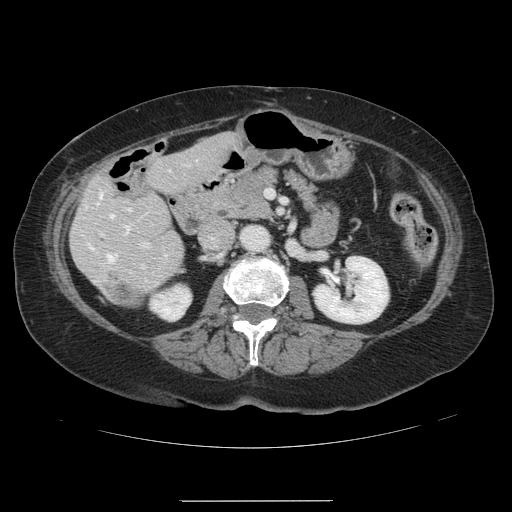
Contrast-enhanced abdominal CT, one axial slice; position 49 of 141 along the scan axis; 120 kVp; intravenous contrast given; soft-tissue window (W 400 / L 40 HU); 2.5 mm slice thickness; 512 × 512 image matrix, field of view 393 × 393 mm. Female patient, age 74 years. Case-level facts recorded for this patient, not image findings: diagnosis: colorectal cancer liver metastases, imaged before liver resection; multiple liver metastases: yes; largest metastasis: 7 cm; disease in both lobes: yes.
Annotated regions visible in this slice (manually delineated by an expert):
- hepatic veins: bounding box <99,193,129,262> (left, top, right, bottom; pixels)
- liver: <71,134,236,308>
- planned liver remnant (the part of the liver to remain after resection): <71,134,236,308>
- portal vein (with intrahepatic branches): <100,208,149,246>
- liver metastasis: <116,286,141,305>